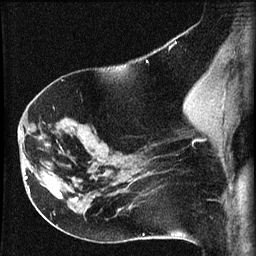
Breast MRI (dynamic contrast-enhanced), one sagittal slice. Slice 38 of 60 in the series (ordered by position). Dynamic contrast-enhanced series, image 2 of 3 at this slice position (ordered by acquisition). 1.5 T. TE 4.2 ms, TR 8.2 ms. 256 × 256 image matrix. Female patient, age 63 years.
Annotated regions visible in this slice (semi-automatic segmentation, software-assisted and operator-edited):
- analysis volume of interest (the breast-tissue region the enhancement analysis was run in; not a lesion): bounding box [x1, y1, x2, y2] px = [22, 156, 64, 202]
- tumour enhancement mask (voxels above the 70 % enhancement threshold inside the analysis volume of interest): [25, 176, 62, 198]